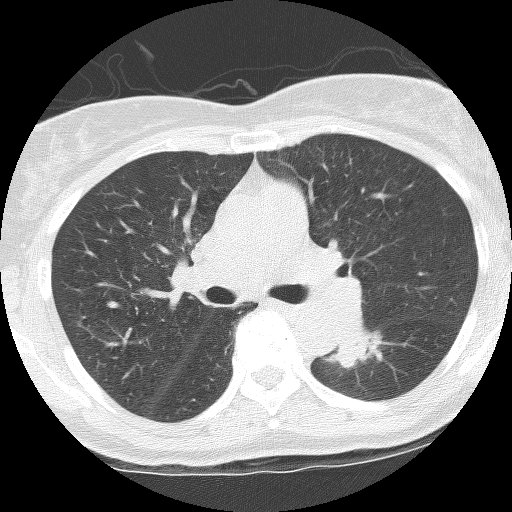
Low-dose screening chest CT, axial slice. Third annual screen. Lung window (W 1500 / L -600 HU). 2.5 mm slice thickness. Lung (sharp) reconstruction kernel (BONE). Slice 48 of 115 in the series. Female, age 62 years at enrolment. Former smoker at enrolment.
• Expert-annotated lung lesion, bounding box [x1, y1, x2, y2] px = [322, 326, 387, 368].
• The screening reader recorded 3 non-calcified nodules or masses ≥4 mm on this exam (right upper lobe, left lower lobe, left upper lobe); which of them this box marks is not recorded.
• Later outcome: lung cancer diagnosed 165 days after this screen — squamous cell carcinoma, NOS, left lower lobe, stage IIIB (AJCC 6th edition), 31 mm at pathology.